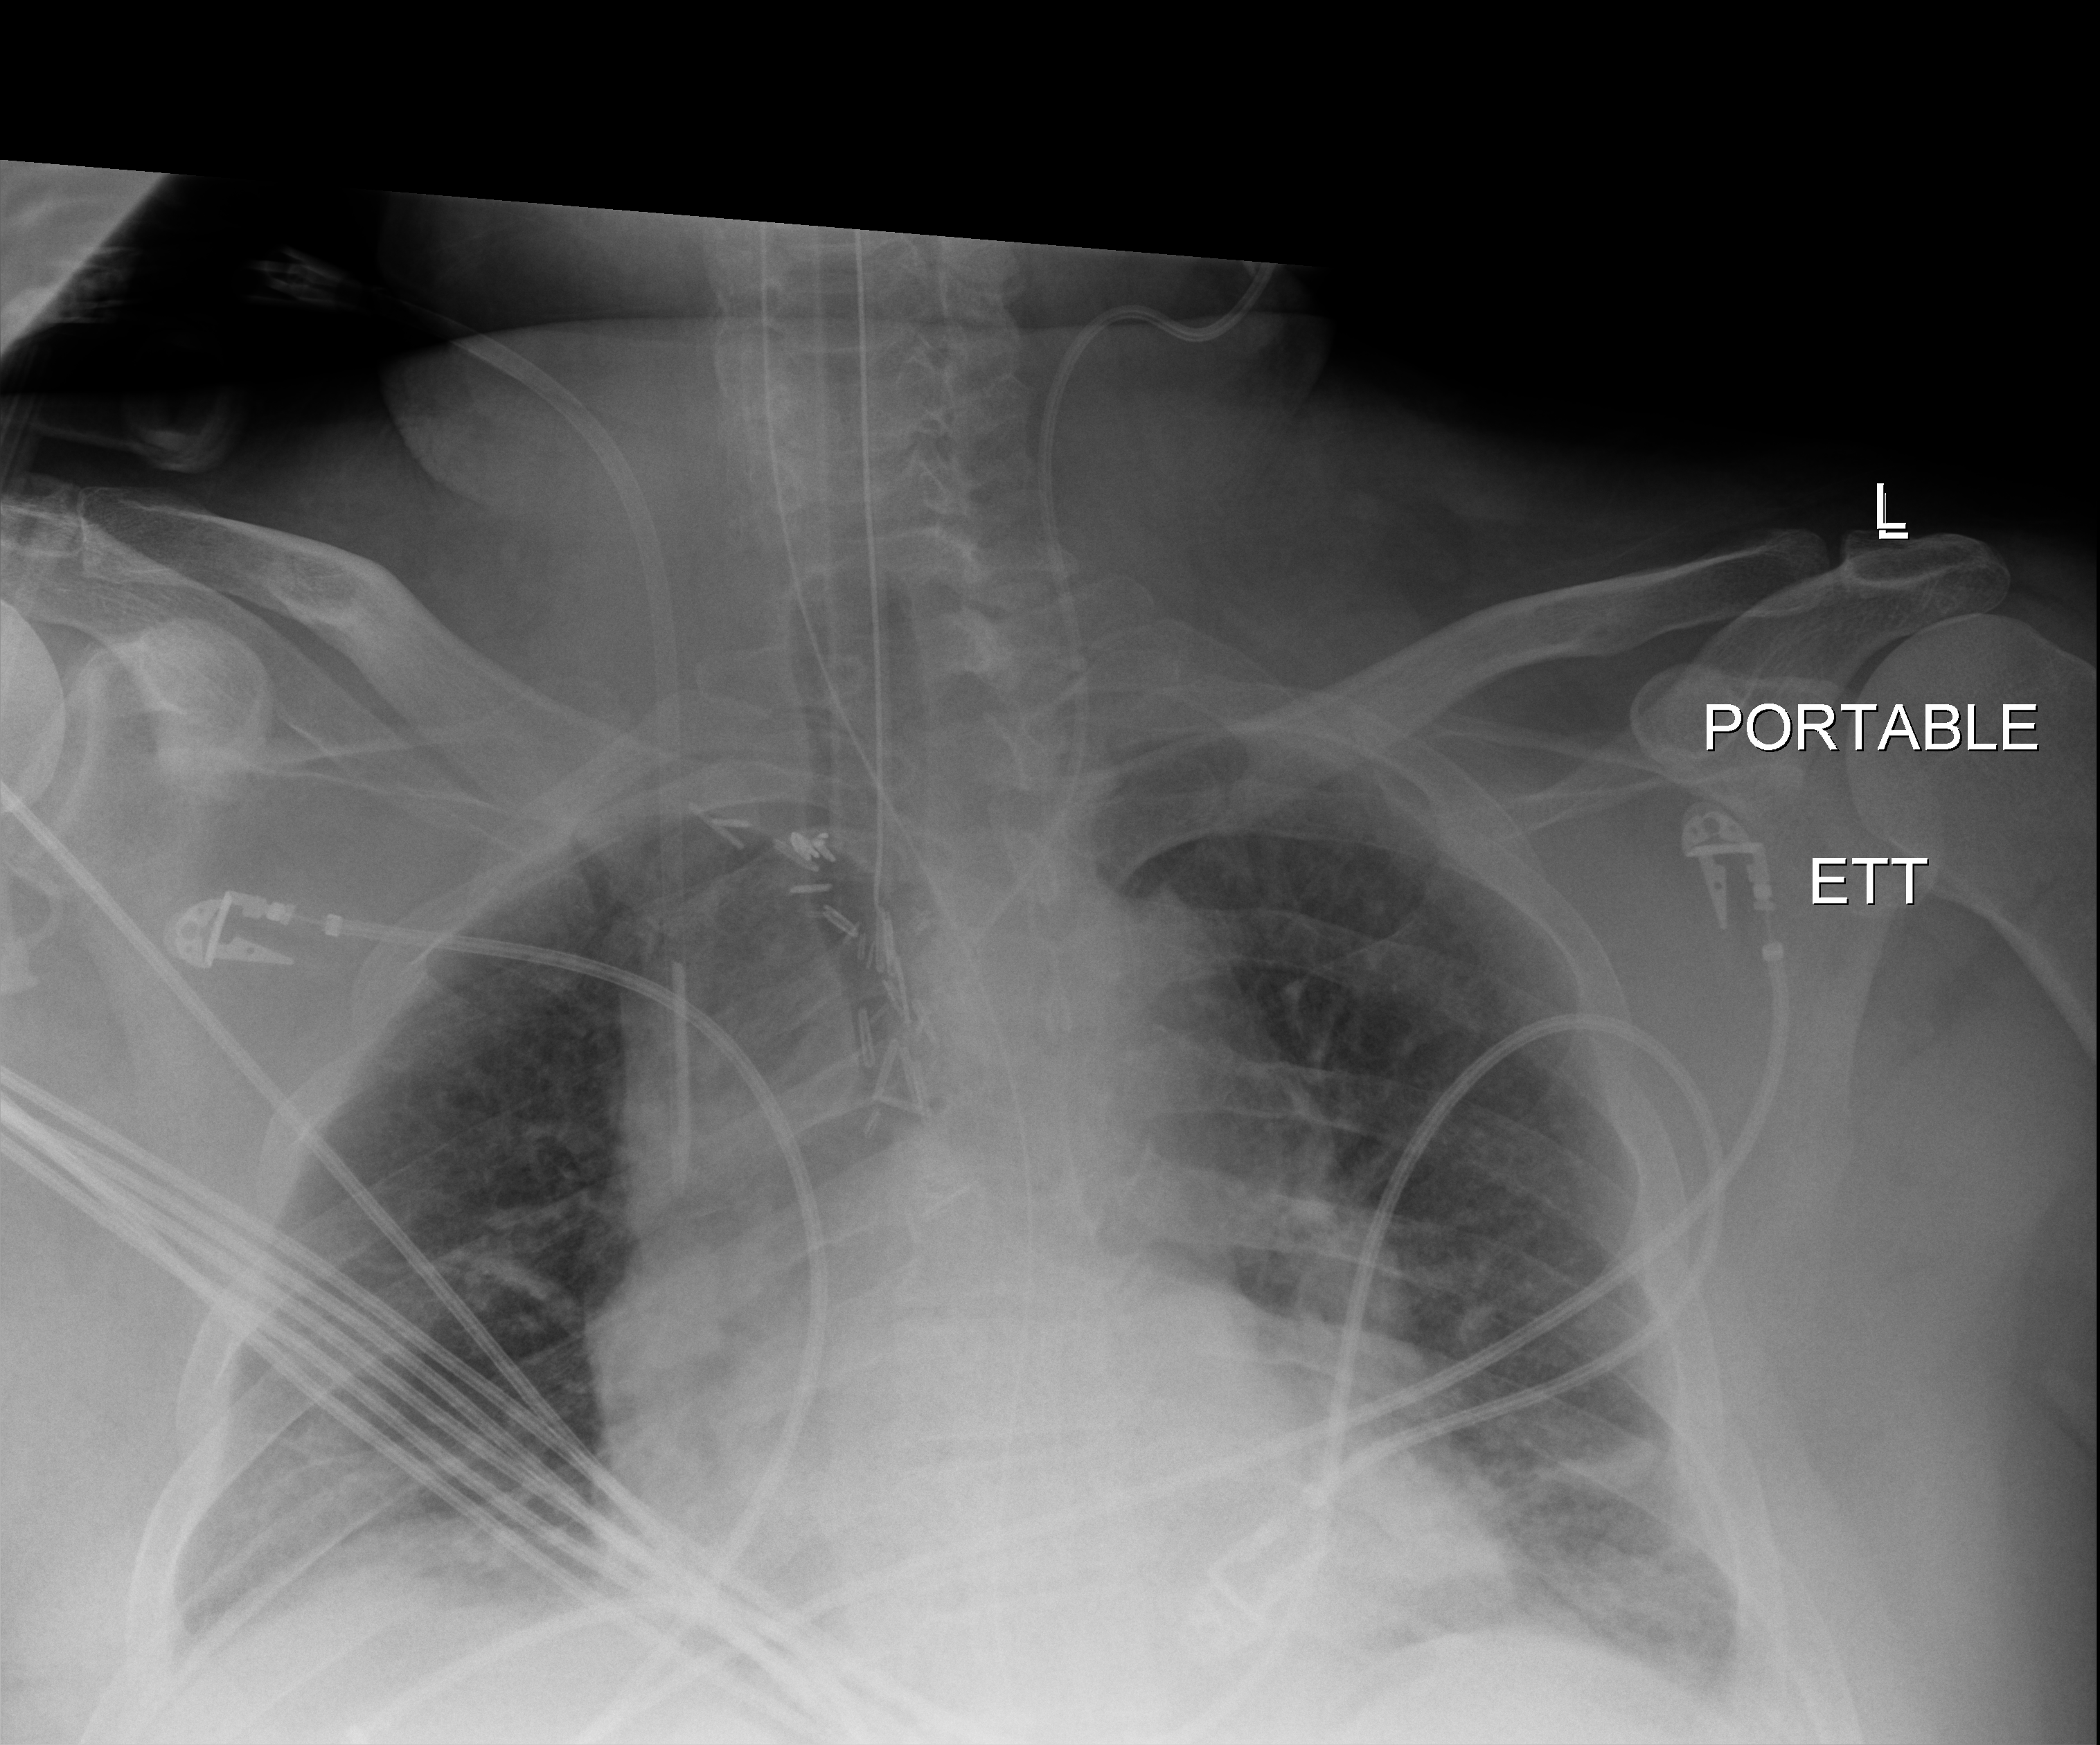
Portable chest radiograph, anteroposterior (AP) projection. Patient hospitalised with COVID-19, aged 18–59 years.
Admission-level facts for this patient (not findings on this image; timing relative to this image not recorded):
- mechanically ventilated during this hospital stay: yes